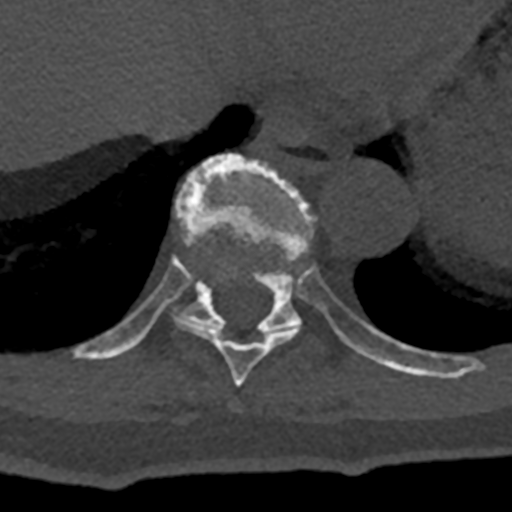
CT including the spine, one axial slice. Position 629 of 797 along the scan axis. Reconstruction kernel Br40s/3. 120 kVp. Bone window (W 1800 / L 400 HU). 0.5 mm slice thickness. 512 × 512 image matrix, field of view 160 × 160 mm. Male patient, age 74 years. From the clinical record (not read from this slice): primary cancer: renal; vertebrae with lytic lesions (as recorded): T10, L1, L2, L3, L4, L5.
Annotated regions visible in this slice (semi-automatically segmented with operator editing):
- T10 vertebra: box from (x=73, y=153) to (x=432, y=377) px
- T9 vertebra: (x=175, y=257)–(x=299, y=387)